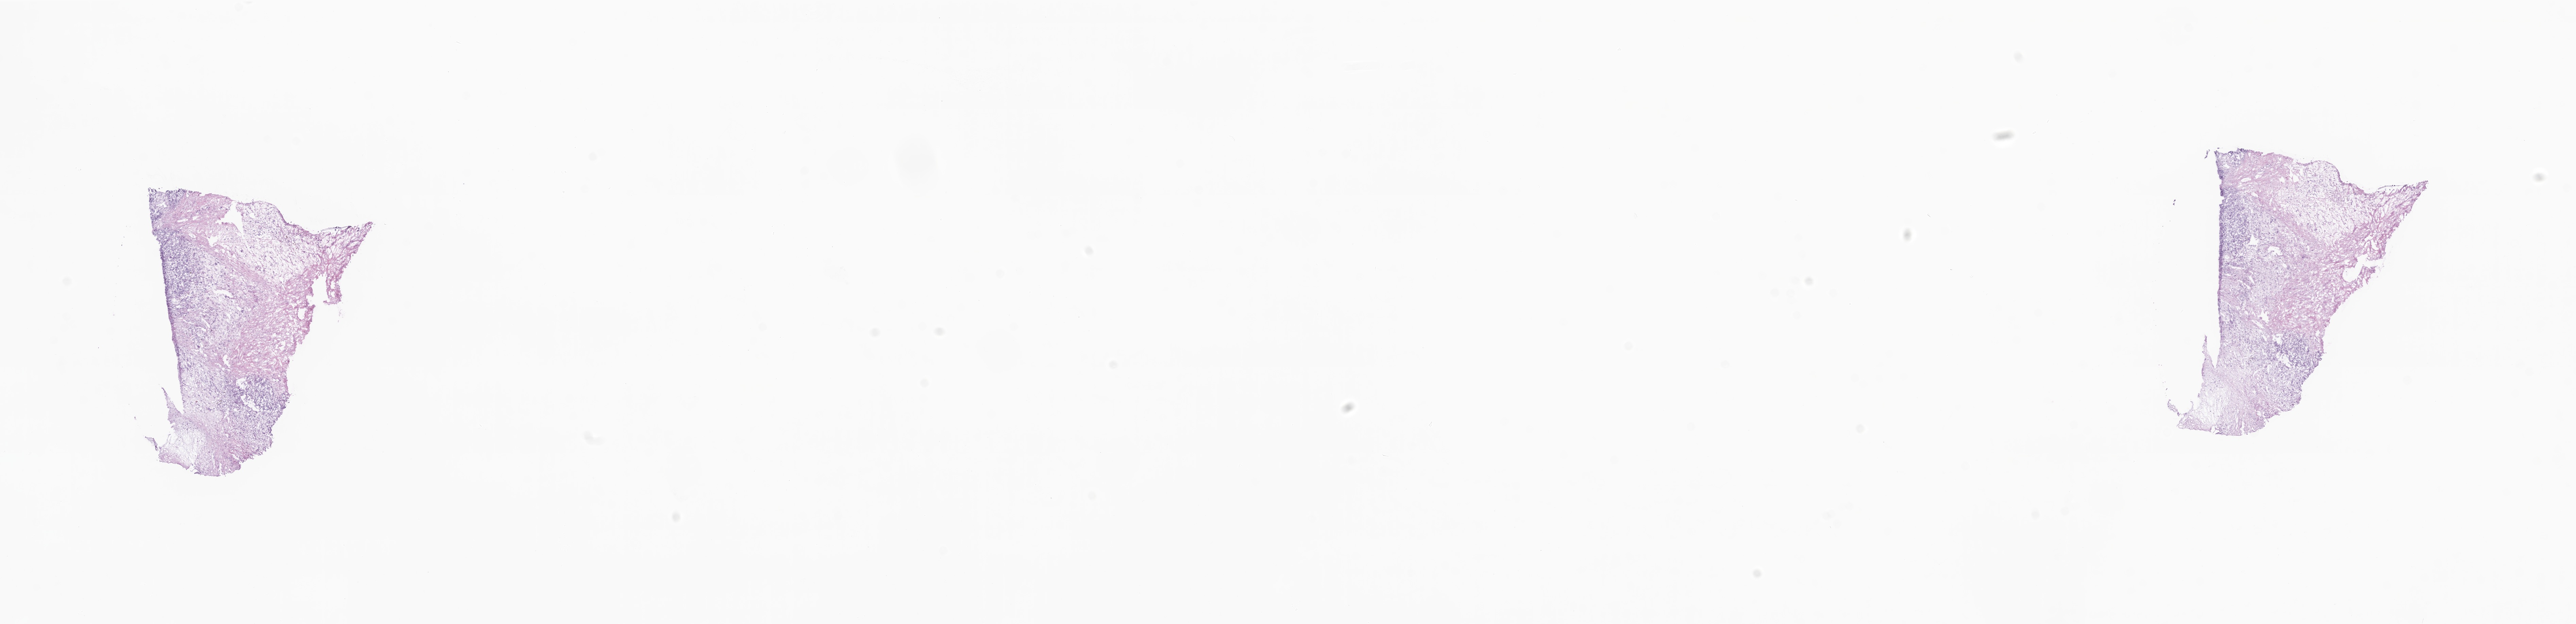
Whole-slide image, hematoxylin and eosin (H&E) stain — shown as a low-resolution overview of the whole scanned area (about 31.9 x 7.7 mm). Frozen section. Primary tumor. Site: body of pancreas. Patient: female, age at initial diagnosis 71 years. Tumor grade: G3 (poorly differentiated). Pathologist review of this section (percent, as recorded): tumor cells 45%, tumor nuclei 85%, stromal cells 47%, necrosis 0%, normal cells 8%. Inflammatory infiltration, as recorded: lymphocyte infiltration 0%, monocyte infiltration 3%, neutrophil infiltration 0%.
Histologic diagnosis: Carcinosarcoma, NOS. AJCC pathologic stage: Stage III.